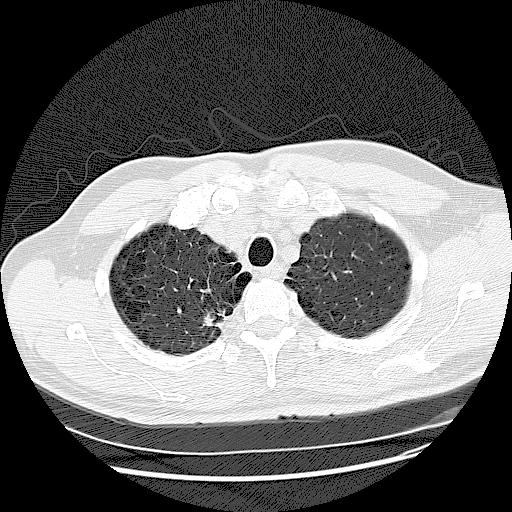
Low-dose screening chest CT, one axial slice. Position 111 of 132 along the scan axis. 120 kVp. Lung window (W 1500 / L -600 HU). 2.5 mm slice thickness. 512 × 512 image matrix.
Annotated regions visible in this slice (expert manual segmentation):
- lesion 1 (tumor, upper lobe of right lung): bounding box [x1, y1, x2, y2] px = [200, 307, 229, 329]